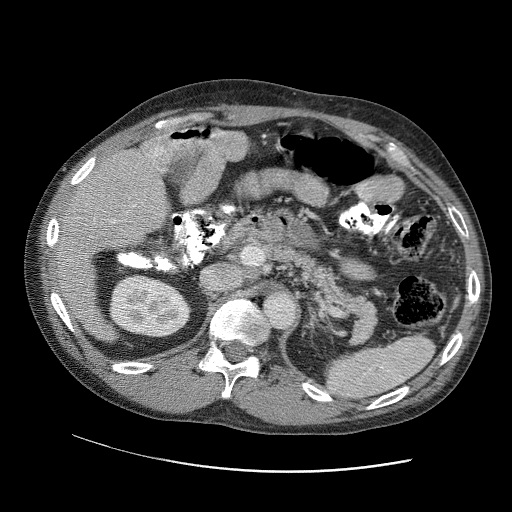
Contrast-enhanced abdominal CT (liver protocol), one axial slice. Position 59 of 109 along the scan axis. Reconstruction kernel STANDARD. Soft-tissue window (W 400 / L 40 HU). 2.5 mm slice thickness. 512 × 512 image matrix, field of view 400 × 400 mm. From the clinical record (not read from this slice): diagnosis: hepatocellular carcinoma (patient treated with transarterial chemoembolisation; whether this scan precedes or follows treatment is not stated here); TNM stage (as recorded): Stage-IIIC; Child-Pugh class: B; tumour nodularity: uninodular.
Outlined on this slice (semi-automatically segmented with operator editing):
- liver parenchyma outside the tumour (the mass and vessels are separate outlines, so this box may not span the whole liver): bounding box (x1, y1, x2, y2) in pixels: (58, 132, 250, 256)
- liver vessels: (74, 133, 247, 225)